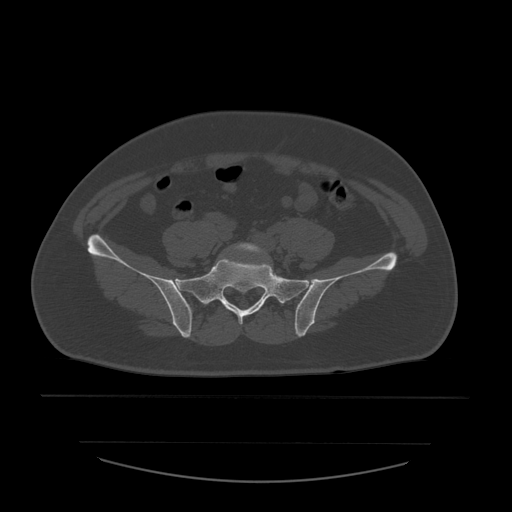
CT including the spine, one axial slice; position 102 of 532 along the scan axis; 120 kVp; bone window (W 1800 / L 400 HU); 512 × 512 image matrix, field of view 441 × 441 mm. Patient age 44 years. Case-level facts recorded for this patient, not image findings: primary cancer: soft tissue sarcoma.
Outlined on this slice (semi-automatic segmentation, software-assisted and operator-edited):
- L5 vertebra: bounding box <234,243,267,256> (left, top, right, bottom; pixels)